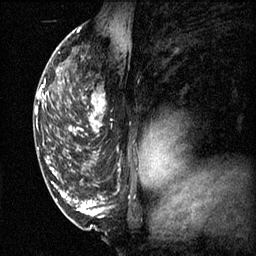
Breast MRI (dynamic contrast-enhanced), one sagittal slice. Slice 36 of 60 in the series (ordered by position). 3 images stored at this slice position (order not interpretable as contrast timing). 1.5 T. TE 4.2 ms, TR 11.1 ms. 2 mm slice thickness. 256 × 256 image matrix, field of view 180 × 180 mm. Female patient, age 50 years.
Outlined on this slice (semi-automatically segmented with operator editing):
- analysis volume of interest (the breast-tissue region the enhancement analysis was run in; not a lesion): box from (x=68, y=68) to (x=113, y=141) px
- tumour enhancement mask (voxels above the 70 % enhancement threshold inside the analysis volume of interest): (x=70, y=94)–(x=106, y=137)